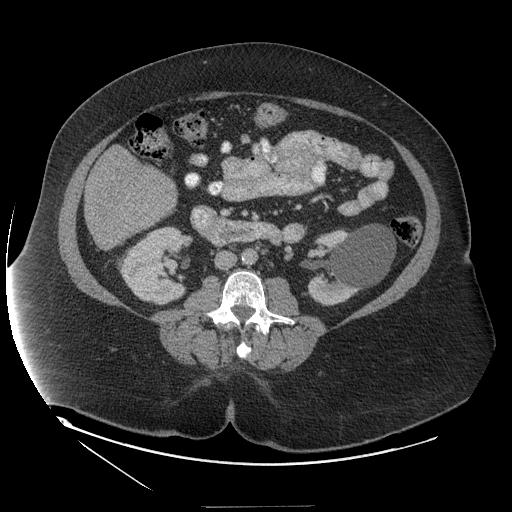
Contrast-enhanced abdominal CT (liver protocol), one axial slice; slice 37 of 127 in the series (ordered by position); reconstruction kernel STANDARD; 140 kVp; soft-tissue window (W 400 / L 40 HU); 2.5 mm slice thickness; 512 × 512 image matrix, field of view 480 × 480 mm. Case-level facts recorded for this patient, not image findings: diagnosis: hepatocellular carcinoma (patient treated with transarterial chemoembolisation; whether this scan precedes or follows treatment is not stated here); TNM stage (as recorded): Stage-II; Child-Pugh class: A; tumour differentiation: well differentiated; tumour nodularity: multinodular.
Outlined on this slice (semi-automatically segmented with operator editing):
- liver parenchyma outside the tumour (the mass and vessels are separate outlines, so this box may not span the whole liver): bounding box <84,169,176,250> (left, top, right, bottom; pixels)